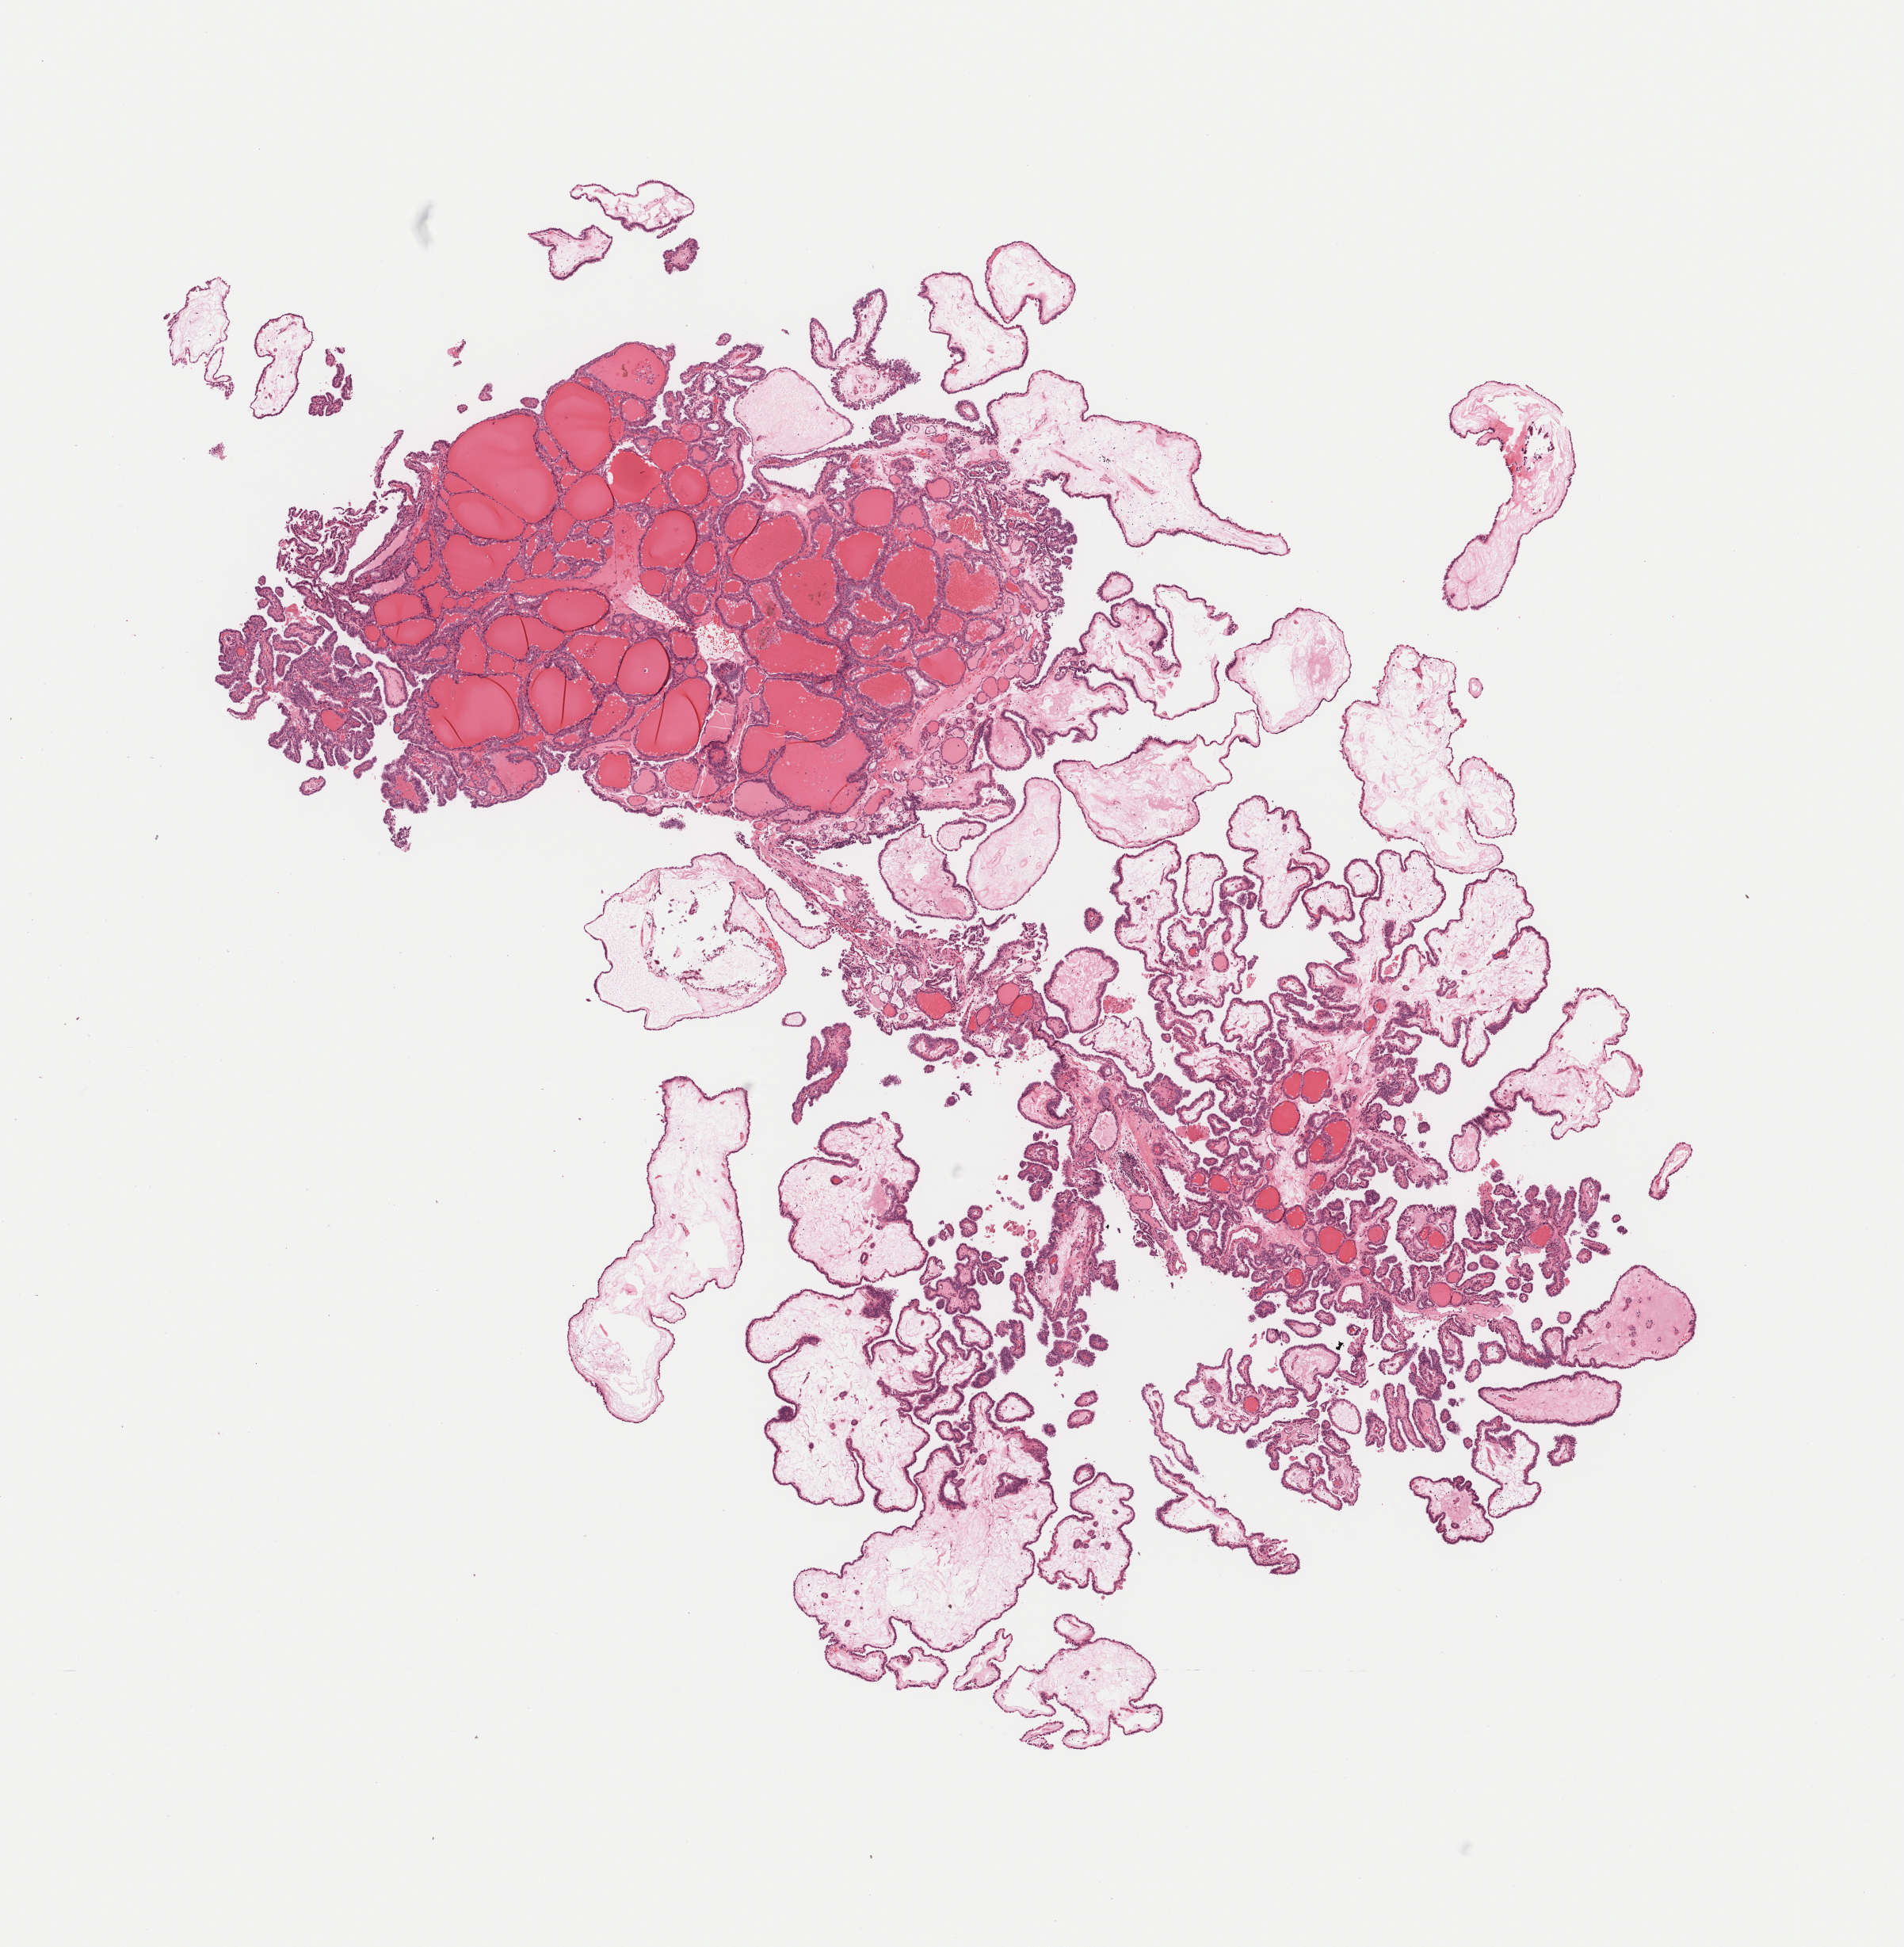
H&E whole-slide image — a low-resolution overview of the entire scanned area, about 9.7 x 9.9 mm (slide scanned at 40x); formalin-fixed paraffin-embedded (FFPE) diagnostic section; sample: primary tumour, thyroid. Male, age 64 years at initial diagnosis.
Lymph nodes positive (case pathology): 14 of 28 examined. AJCC pathologic stage: IVA (7th edition). Pathologic diagnosis: Papillary adenocarcinoma, NOS (thyroid gland).